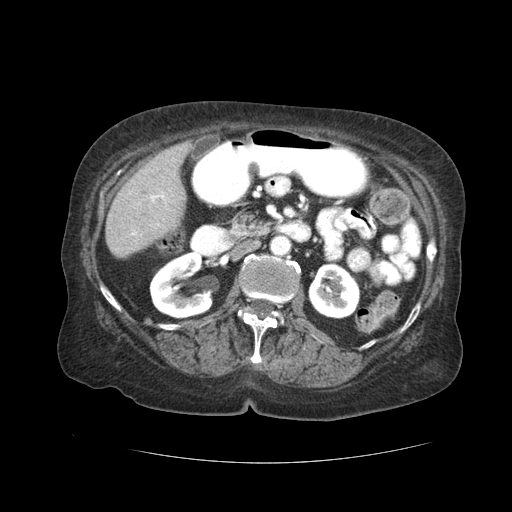
Contrast-enhanced abdominal CT (liver protocol), one axial slice; position 5 of 59 along the scan axis; 120 kVp; soft-tissue window (W 400 / L 40 HU); 2.5 mm slice thickness; 512 × 512 image matrix. Case-level facts recorded for this patient, not image findings: diagnosis: hepatocellular carcinoma (patient treated with transarterial chemoembolisation; whether this scan precedes or follows treatment is not stated here); TNM stage (as recorded): Stage-I; Child-Pugh class: A.
Structures marked on this image (semi-automatic segmentation, software-assisted and operator-edited):
- liver parenchyma outside the tumour (the mass and vessels are separate outlines, so this box may not span the whole liver): bounding box (x1, y1, x2, y2) in pixels: (106, 142, 192, 258)
- liver vessels: (133, 195, 164, 235)